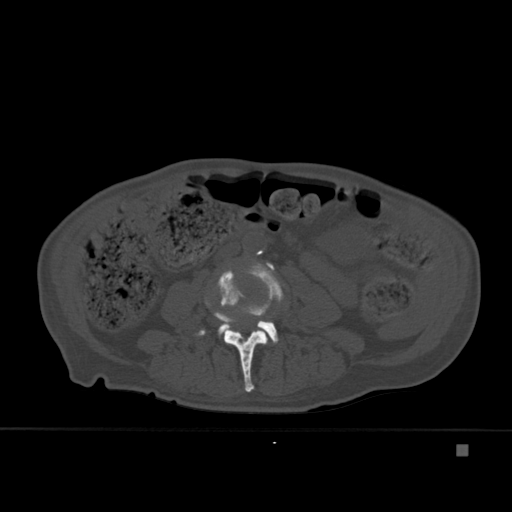
CT including the spine, one axial slice. Bone window (W 1800 / L 400 HU). 1.5 mm slice thickness. 512 × 512 image matrix, field of view 378 × 378 mm. Patient: male, 75 years. From the clinical record (not read from this slice): primary cancer: prostate.
Structures marked on this image (semi-automatic segmentation, software-assisted and operator-edited):
- L3 vertebra: bounding box <196,270,268,392> (left, top, right, bottom; pixels)
- L4 vertebra: <218,262,284,344>